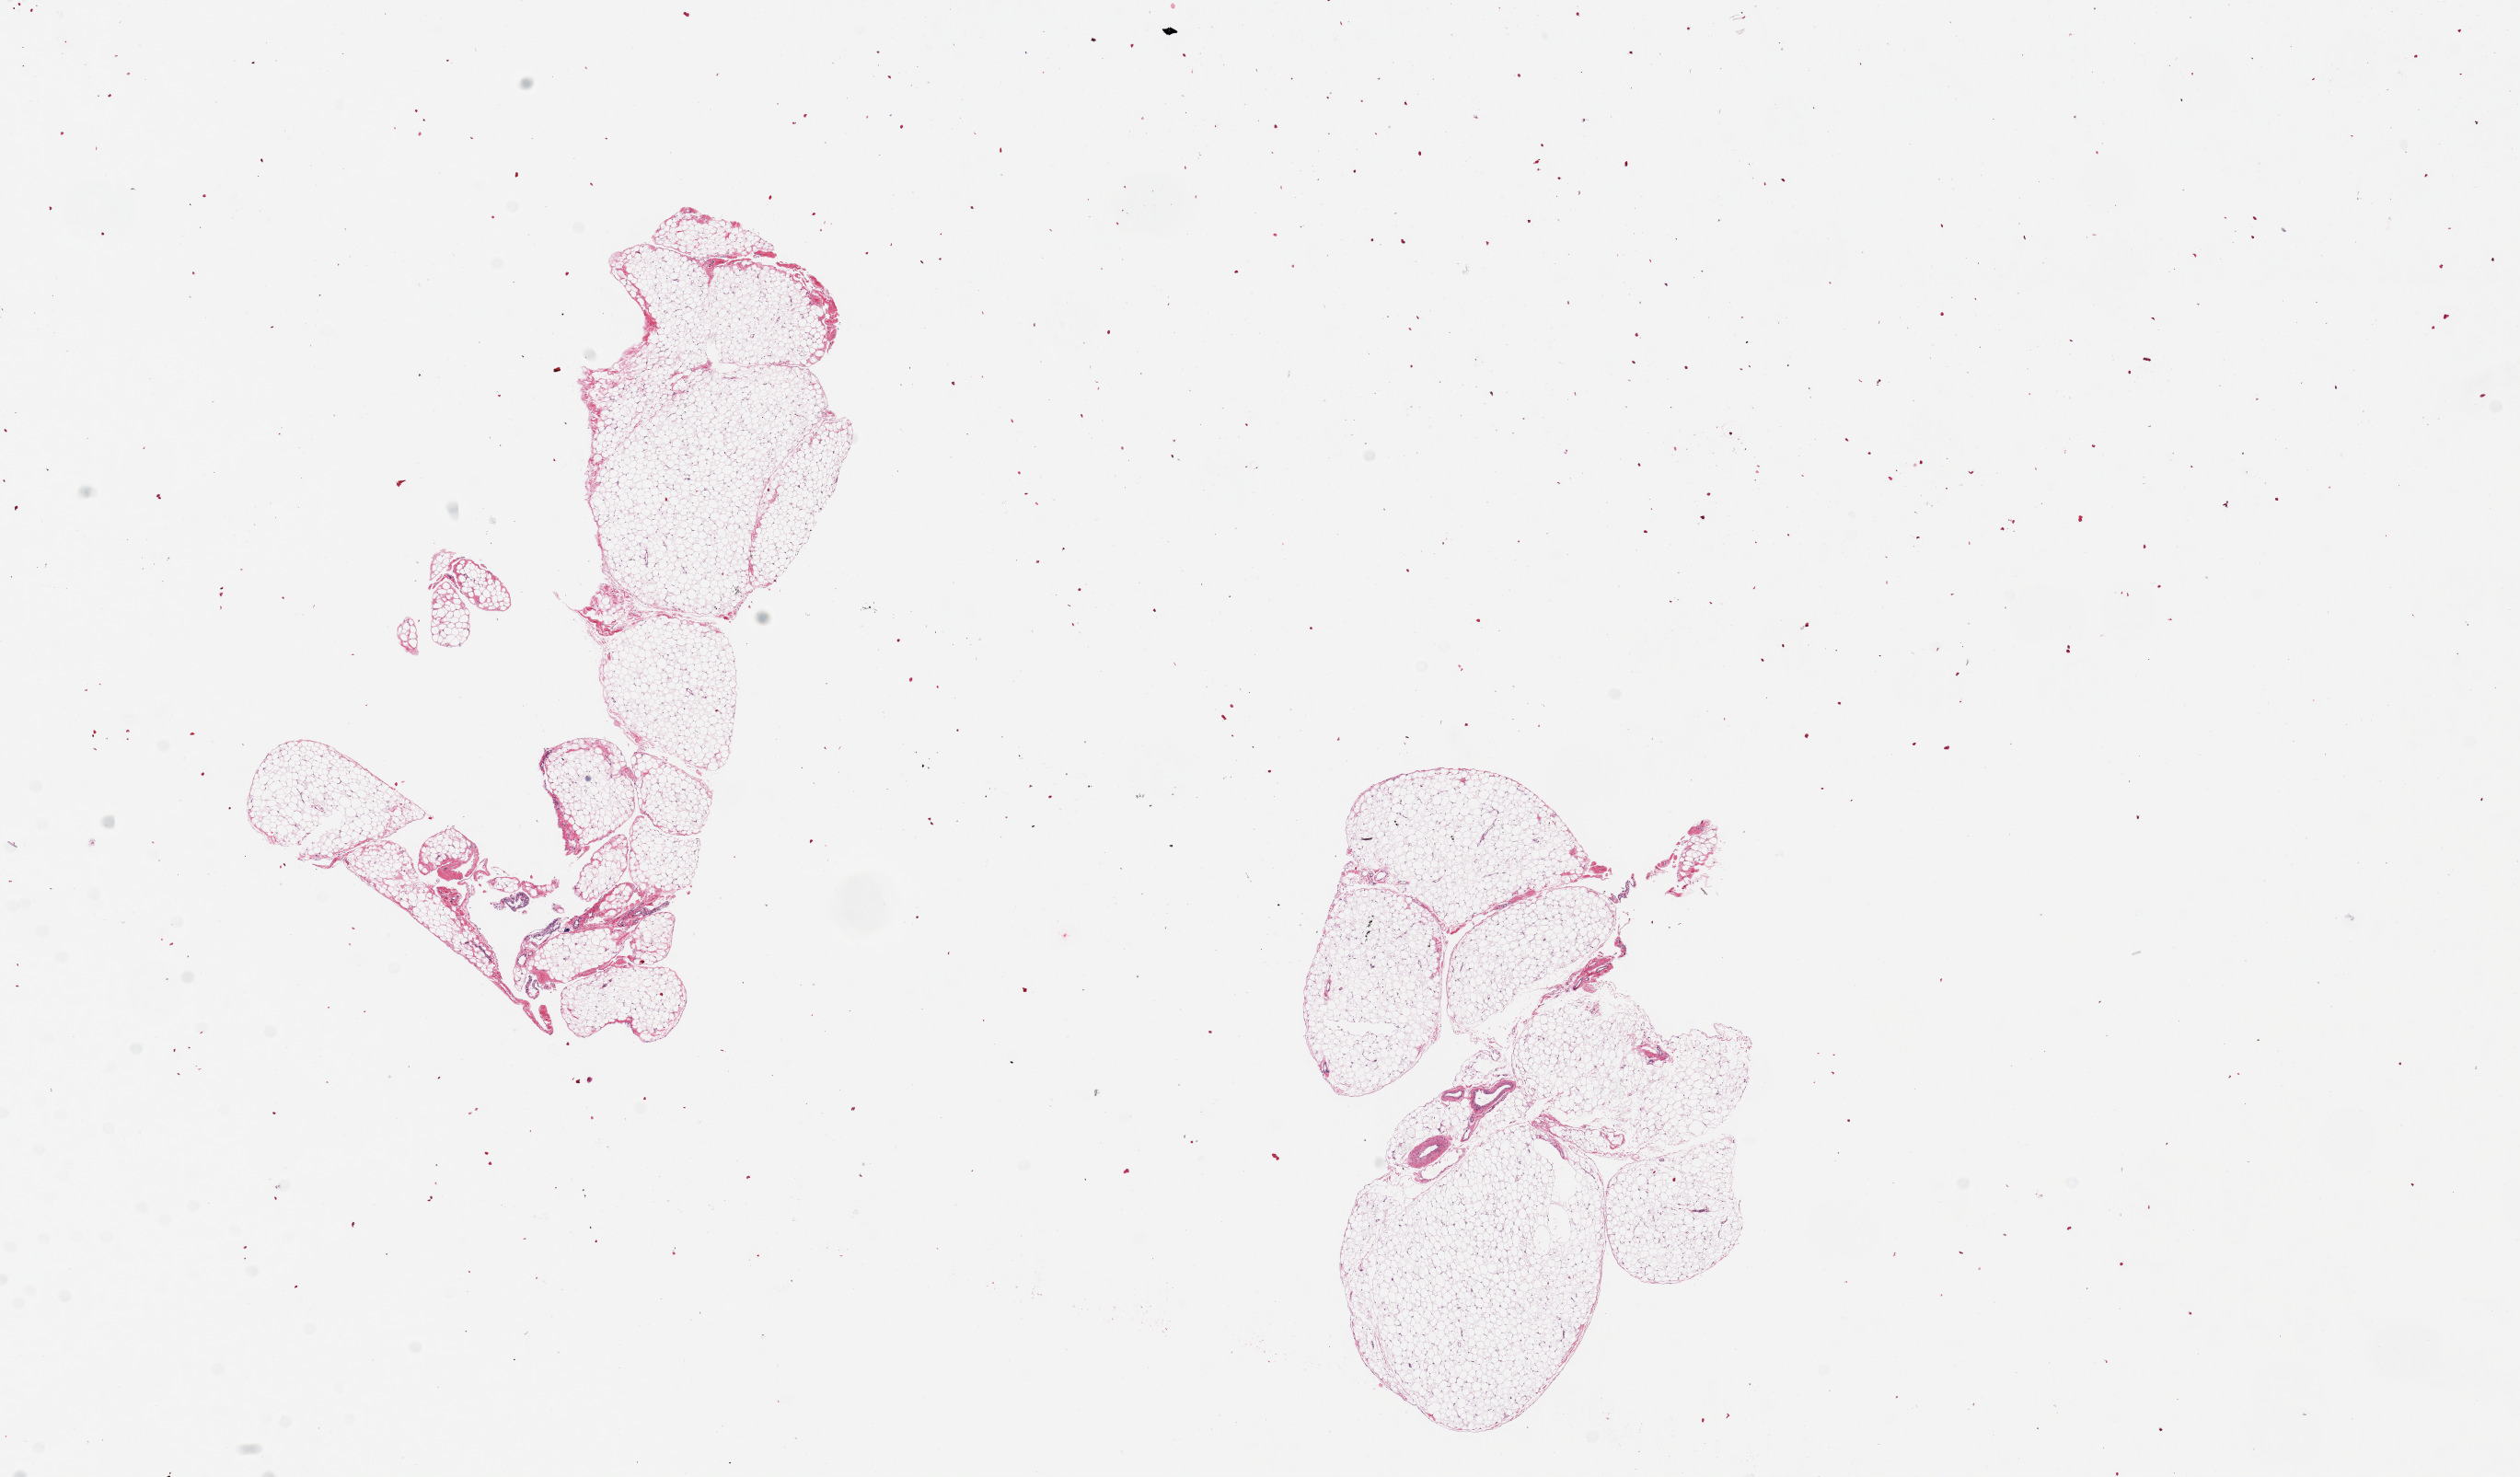
Digitized hematoxylin and eosin (H&E)-stained section — whole scanned area (about 21.7 x 12.7 mm) shown as a low-resolution overview, PAXgene-fixed paraffin-embedded (PFPE) section, target tissue: omentum, tissue donor sample. Female donor.
• reviewer comment on this tissue sample: 2 pieces, 7x4 & 5x4mm